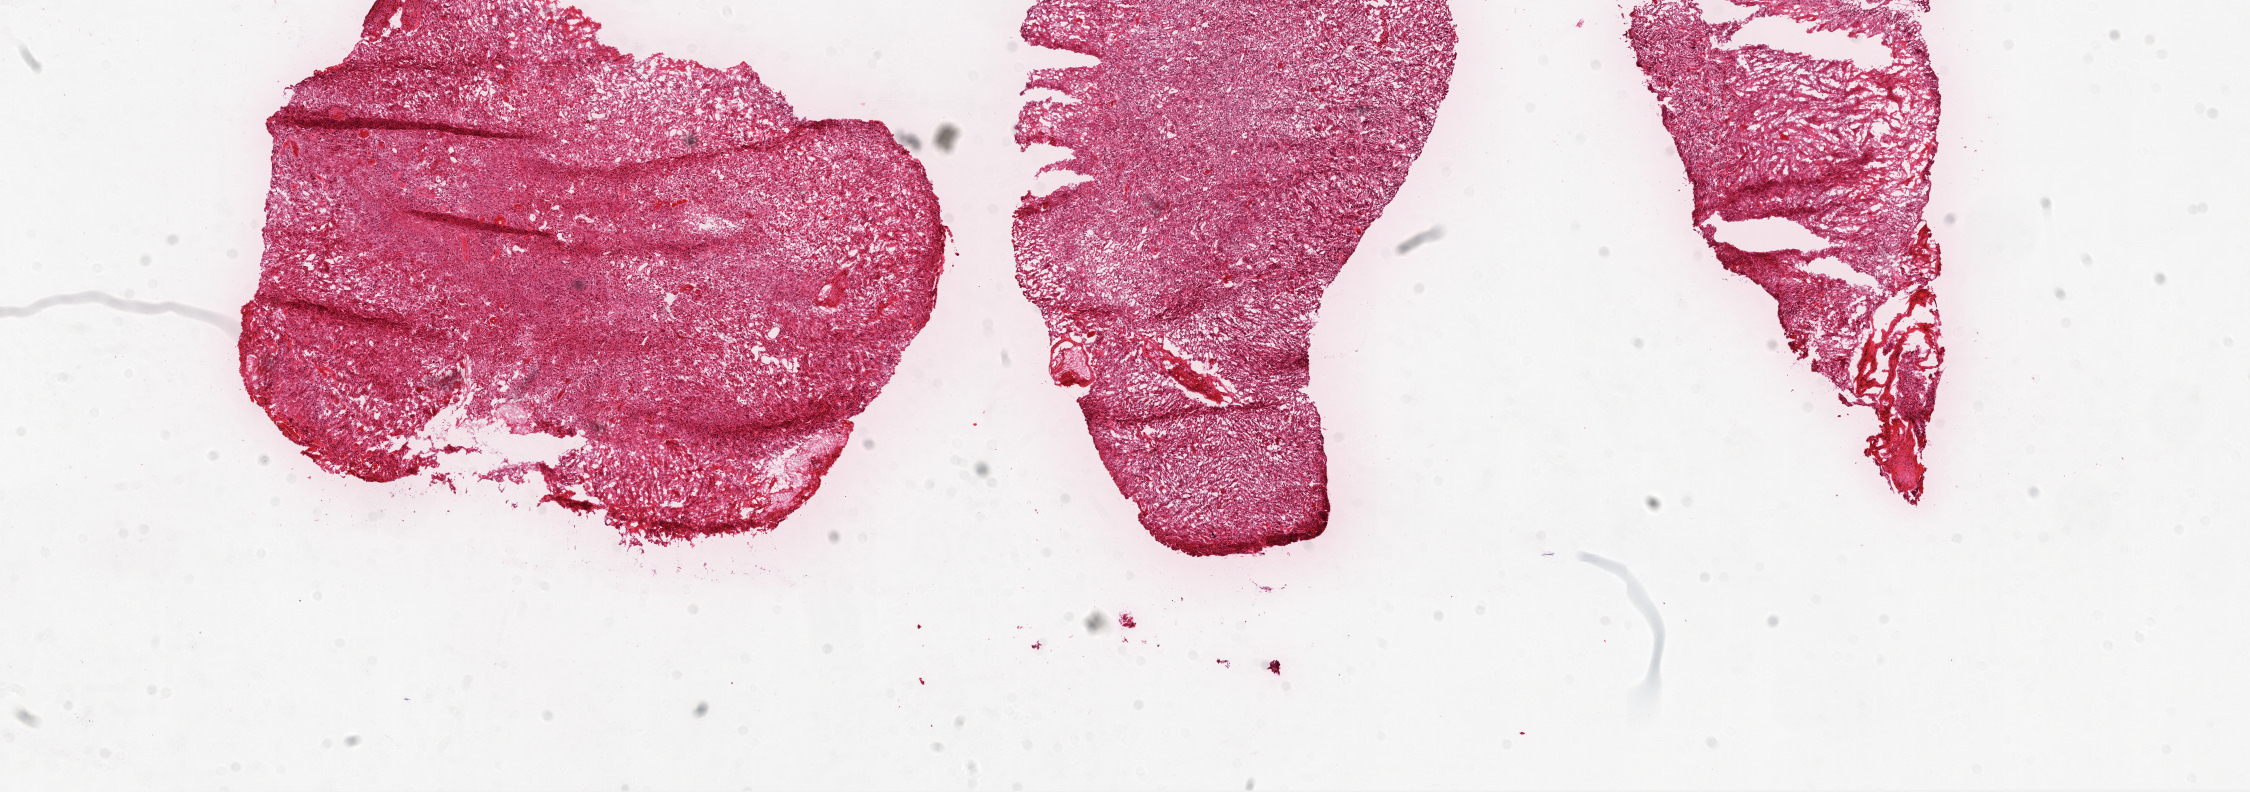
Whole-slide histology image, H&E, a low-resolution overview of the entire scanned area, about 18.1 x 6.4 mm (from a 20x scan). Frozen section from the top of the tissue portion. Brain, primary tumour sample. Female patient; age at initial diagnosis 57 years. Slide review estimates, as recorded: tumour cells 94%, tumour nuclei 85%, normal cells 0%, stromal cells 5%, necrosis 1%.
• pathologic diagnosis: Glioblastoma